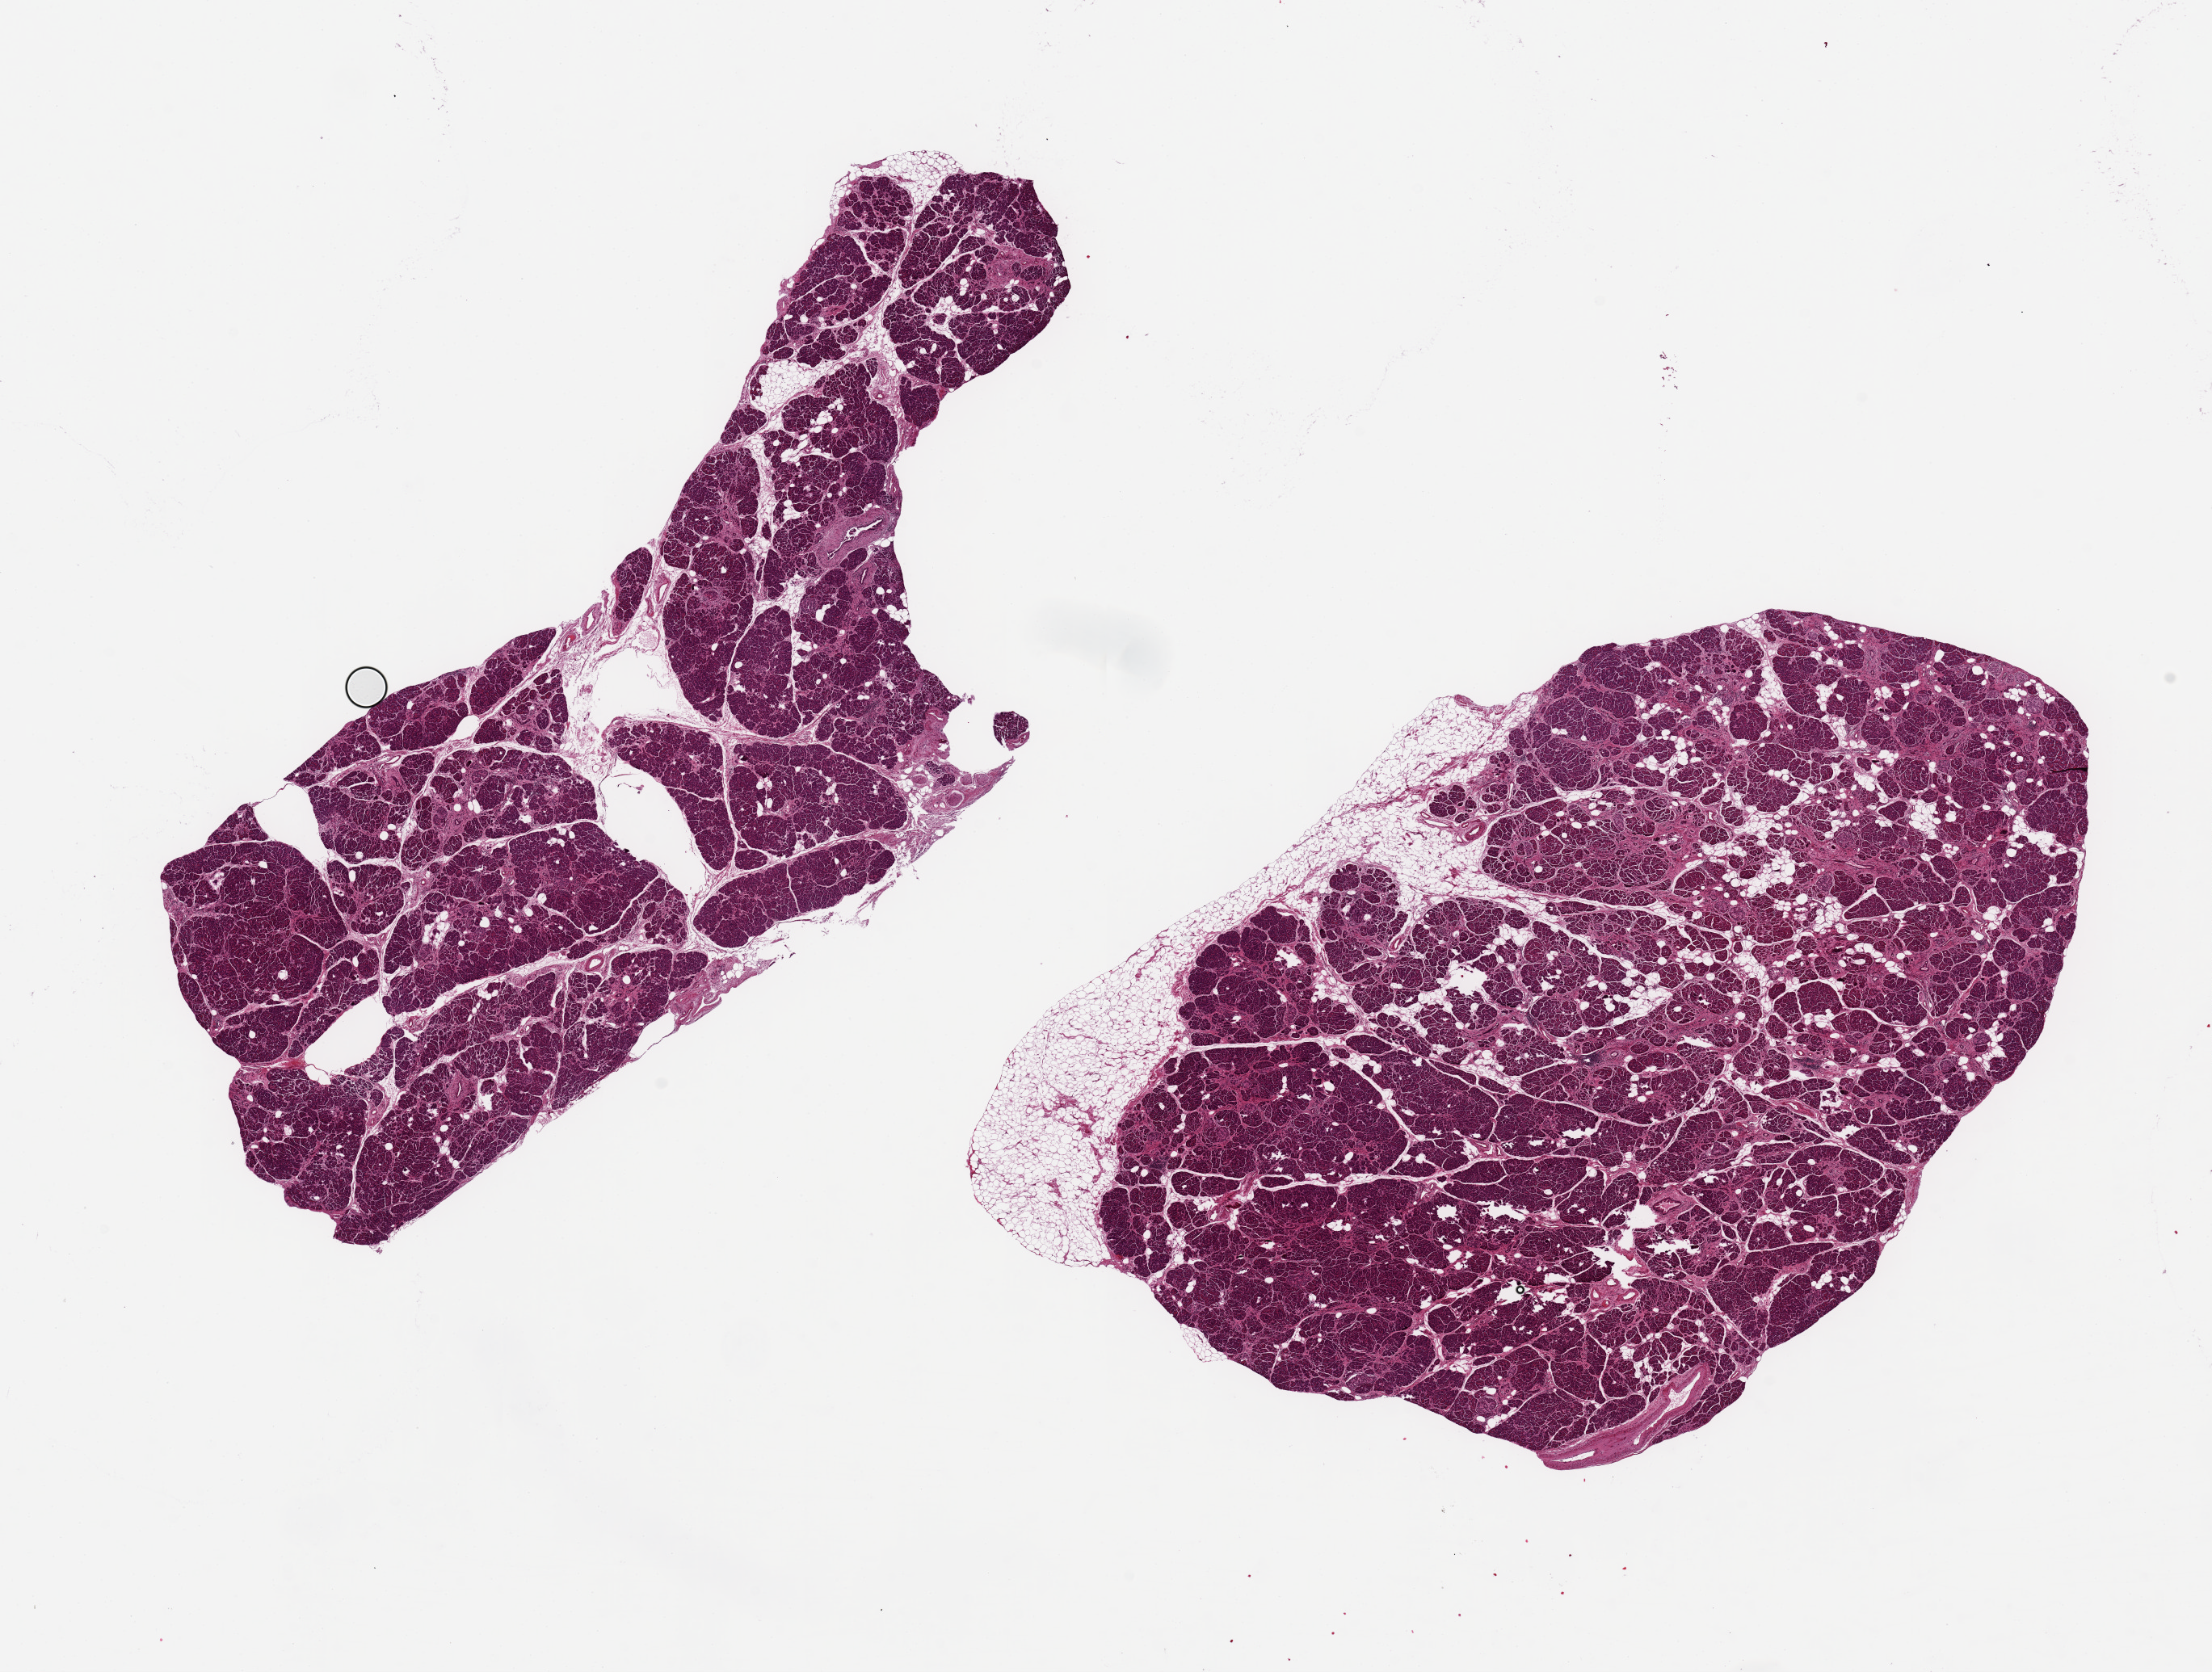
Whole-slide image, haematoxylin and eosin stain — whole scanned area (about 21.7 x 16.4 mm) shown as a low-resolution overview, PAXgene-fixed, paraffin-embedded tissue, sampled site (target tissue): pancreas, donor tissue sample. Male donor.
• reviewer comment on this tissue sample: 2 pieces 11x4 & 9x7 mm; mild patchy fibrosis; ~10% adipose at one edge; scattered adipose in parenchyma